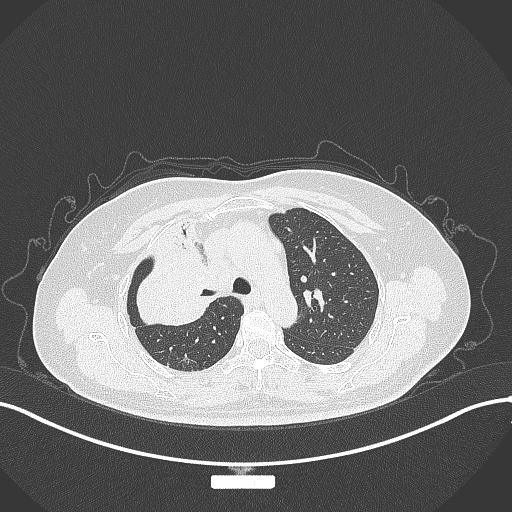
Chest CT, one axial slice. Slice 221 of 309 in the series (ordered by position). Lung window (W 1500 / L -600 HU). 512 × 512 image matrix, field of view 400 × 400 mm. Patient: female, 60 years. Case-level facts recorded for this patient, not image findings: clinical TNM (as recorded): T3 N1 M1.
Outlined on this slice (bounding box drawn by a radiologist):
- lung tumour (recorded histology: adenocarcinoma): bounding box (x1, y1, x2, y2) in pixels: (126, 234, 215, 331)